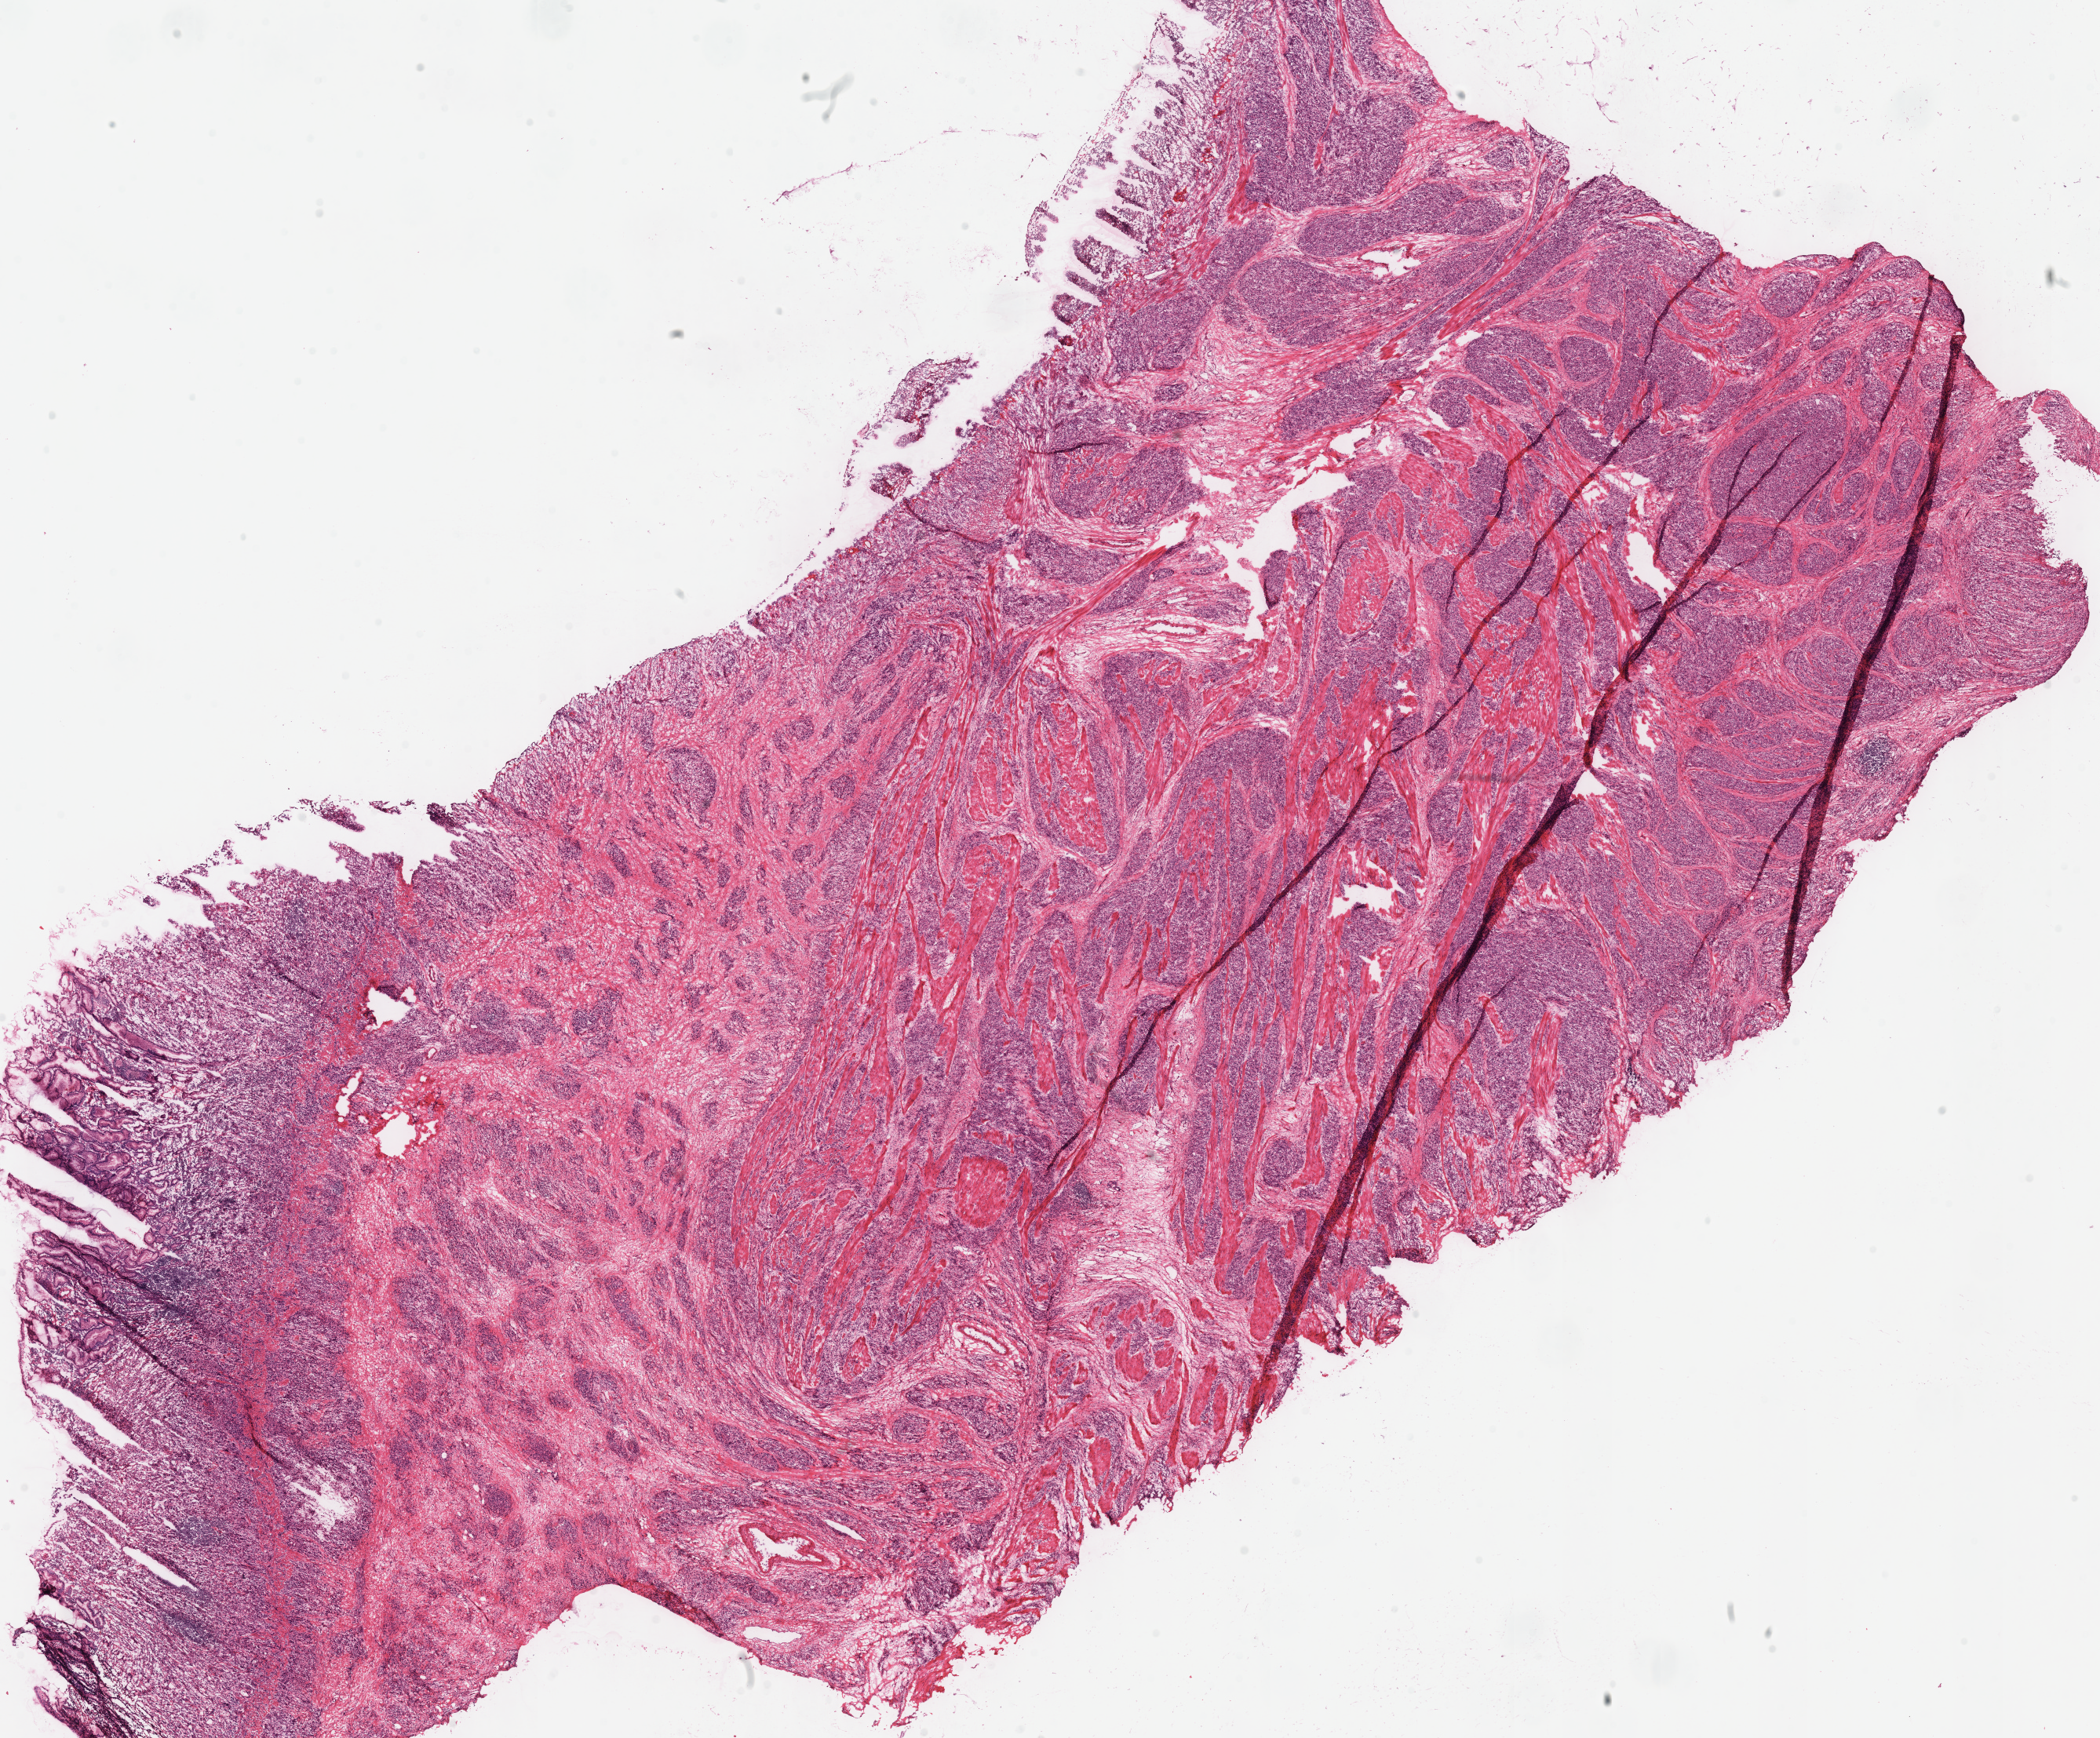
Whole-slide histology image, H&E, shown as a low-resolution overview of the whole scanned area (about 21.0 x 17.4 mm). Frozen section from the top of the tissue portion. Primary tumour sample from the stomach. Male patient; age at initial diagnosis 55 years. Histologic grade: G3 (poorly differentiated). Composition of this section per pathologist review: tumour cells 65%, tumour nuclei 75%, normal cells 10%, stromal cells 25%, necrosis 0%.
• AJCC pathologic stage: IIIB (7th edition)
• diagnosis: Adenocarcinoma, NOS (fundus of stomach)
• lymph nodes positive (case pathology): 9 of 15 examined